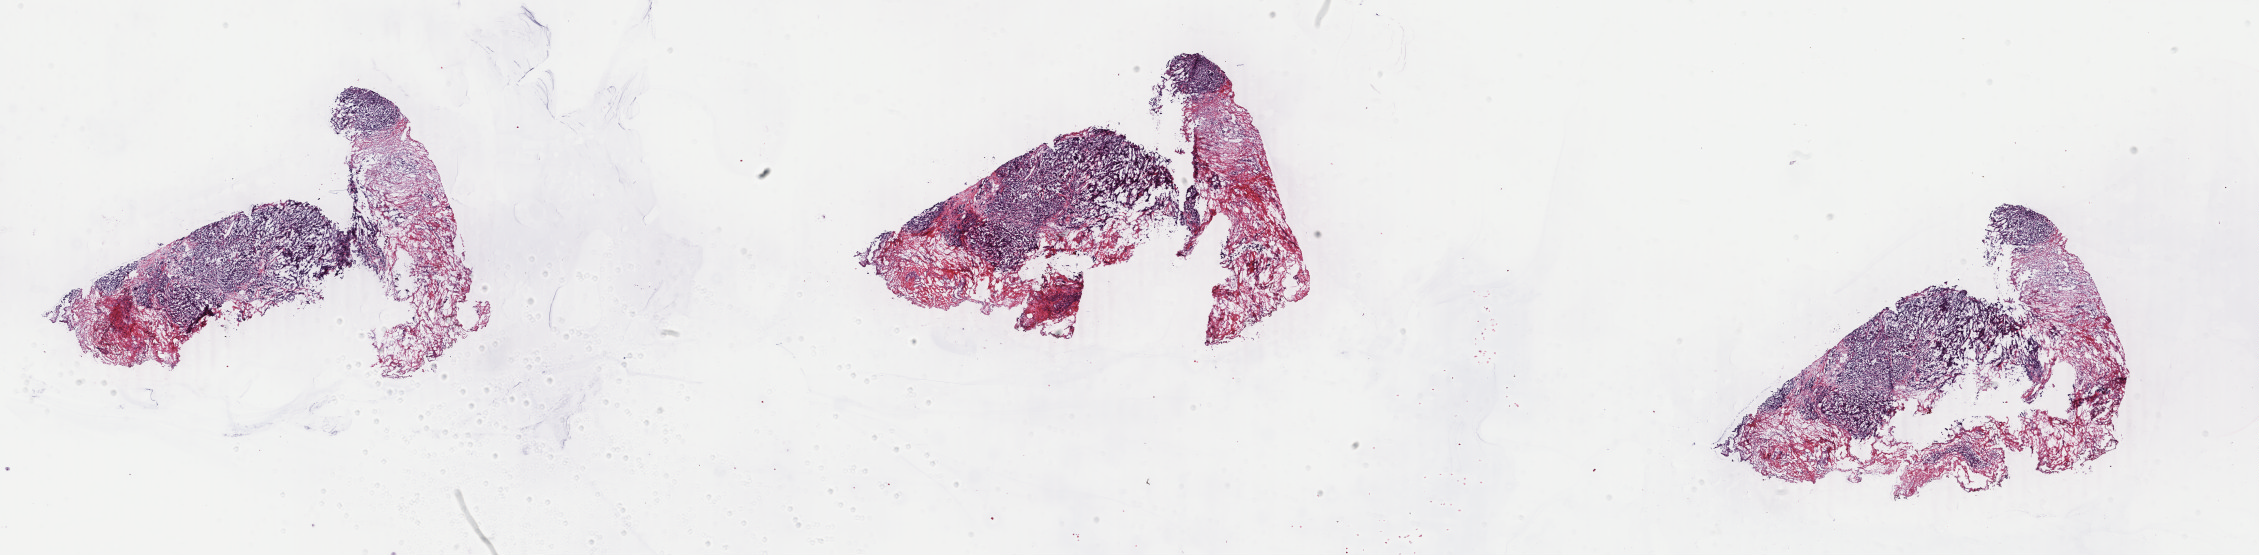
Digitized H&E tissue section (whole slide), shown as a low-resolution overview of the whole scanned area (about 35.9 x 8.8 mm). Frozen section from the bottom of the tissue portion. Breast, primary tumour sample. Patient: female, age at initial diagnosis 56 years. Slide review estimates, as recorded: tumour cells 60%, tumour nuclei 70%, normal cells 0%, stromal cells 40%, necrosis 0%. Inflammatory infiltration, as recorded: lymphocyte infiltration 0%, monocyte infiltration 0%, neutrophil infiltration 0%.
Lymph nodes positive (case pathology): 0 of 10 examined. AJCC pathologic stage: IIA. Laterality: left. Histologic diagnosis: Infiltrating duct carcinoma, NOS.